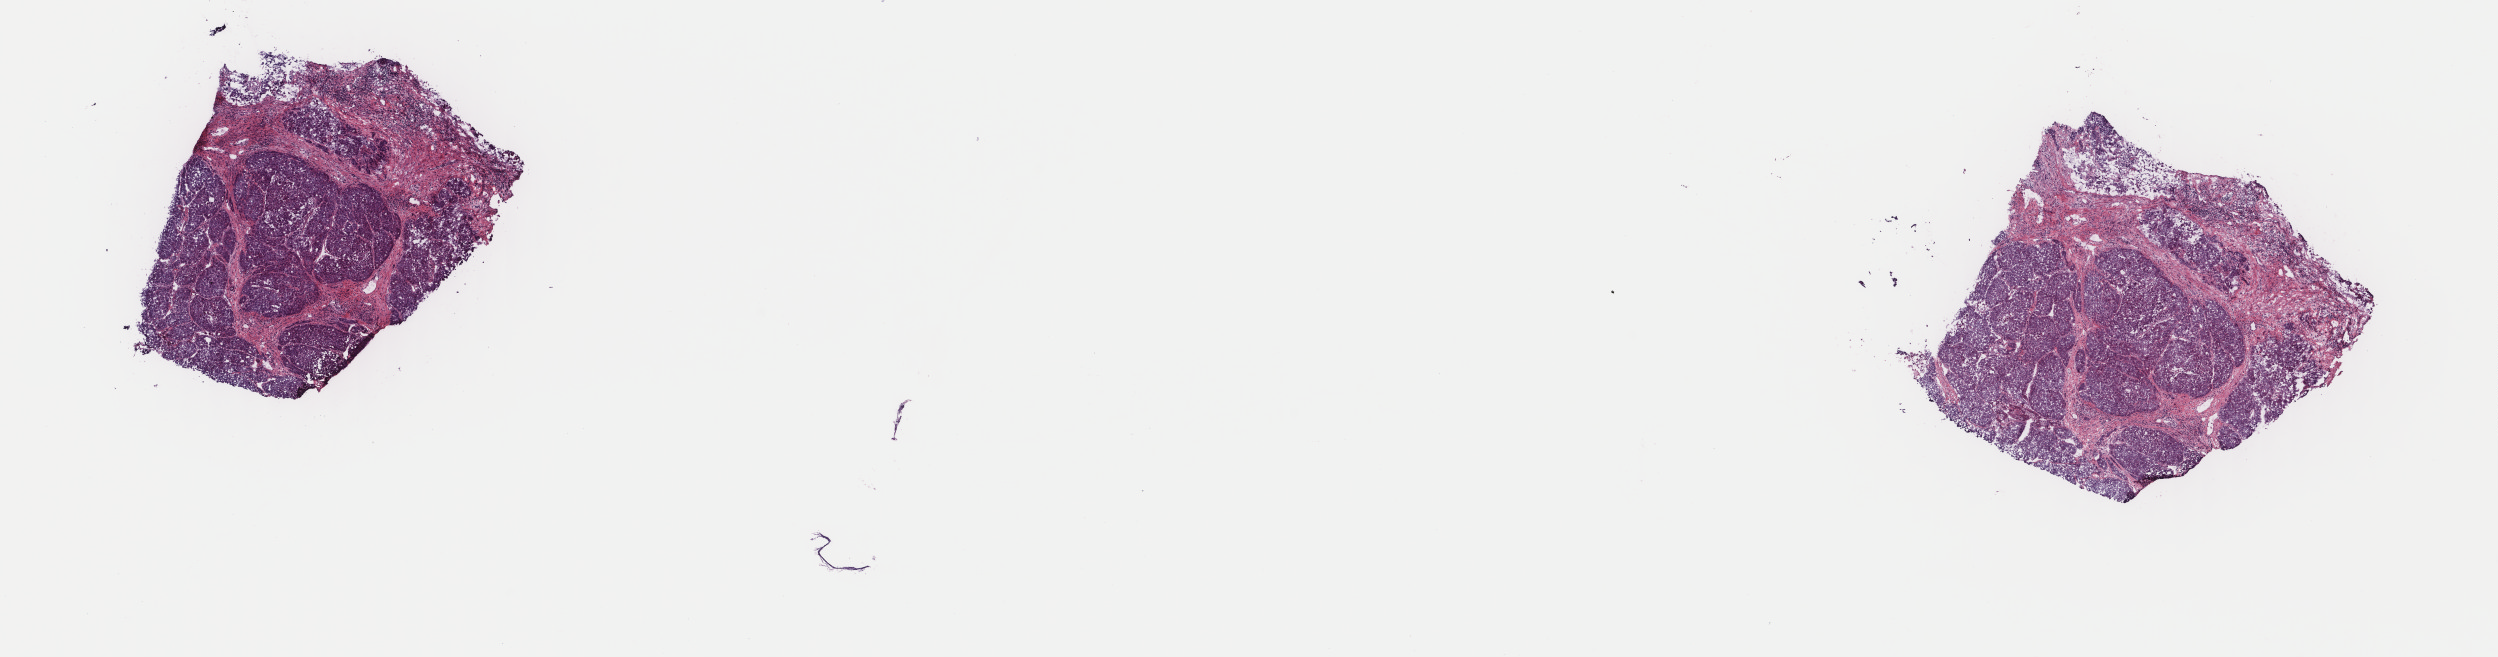
Whole-slide histology image, H&E, whole scanned area (about 19.8 x 5.2 mm, slide scanned at 40x) shown as a low-resolution overview. Frozen section. Primary tumour sample from the liver. Patient: male, age at initial diagnosis 75 years. Histologic grade: G3 (poorly differentiated). Pathologist review of this section (percent, as recorded): tumour cells 62%, tumour nuclei 85%, normal cells 0%, stromal cells 35%, necrosis 3%. Infiltration values recorded for this section: lymphocyte infiltration 10%, monocyte infiltration 0%, neutrophil infiltration 0%.
AJCC pathologic stage: II. Histologic diagnosis: Hepatocellular carcinoma, NOS.